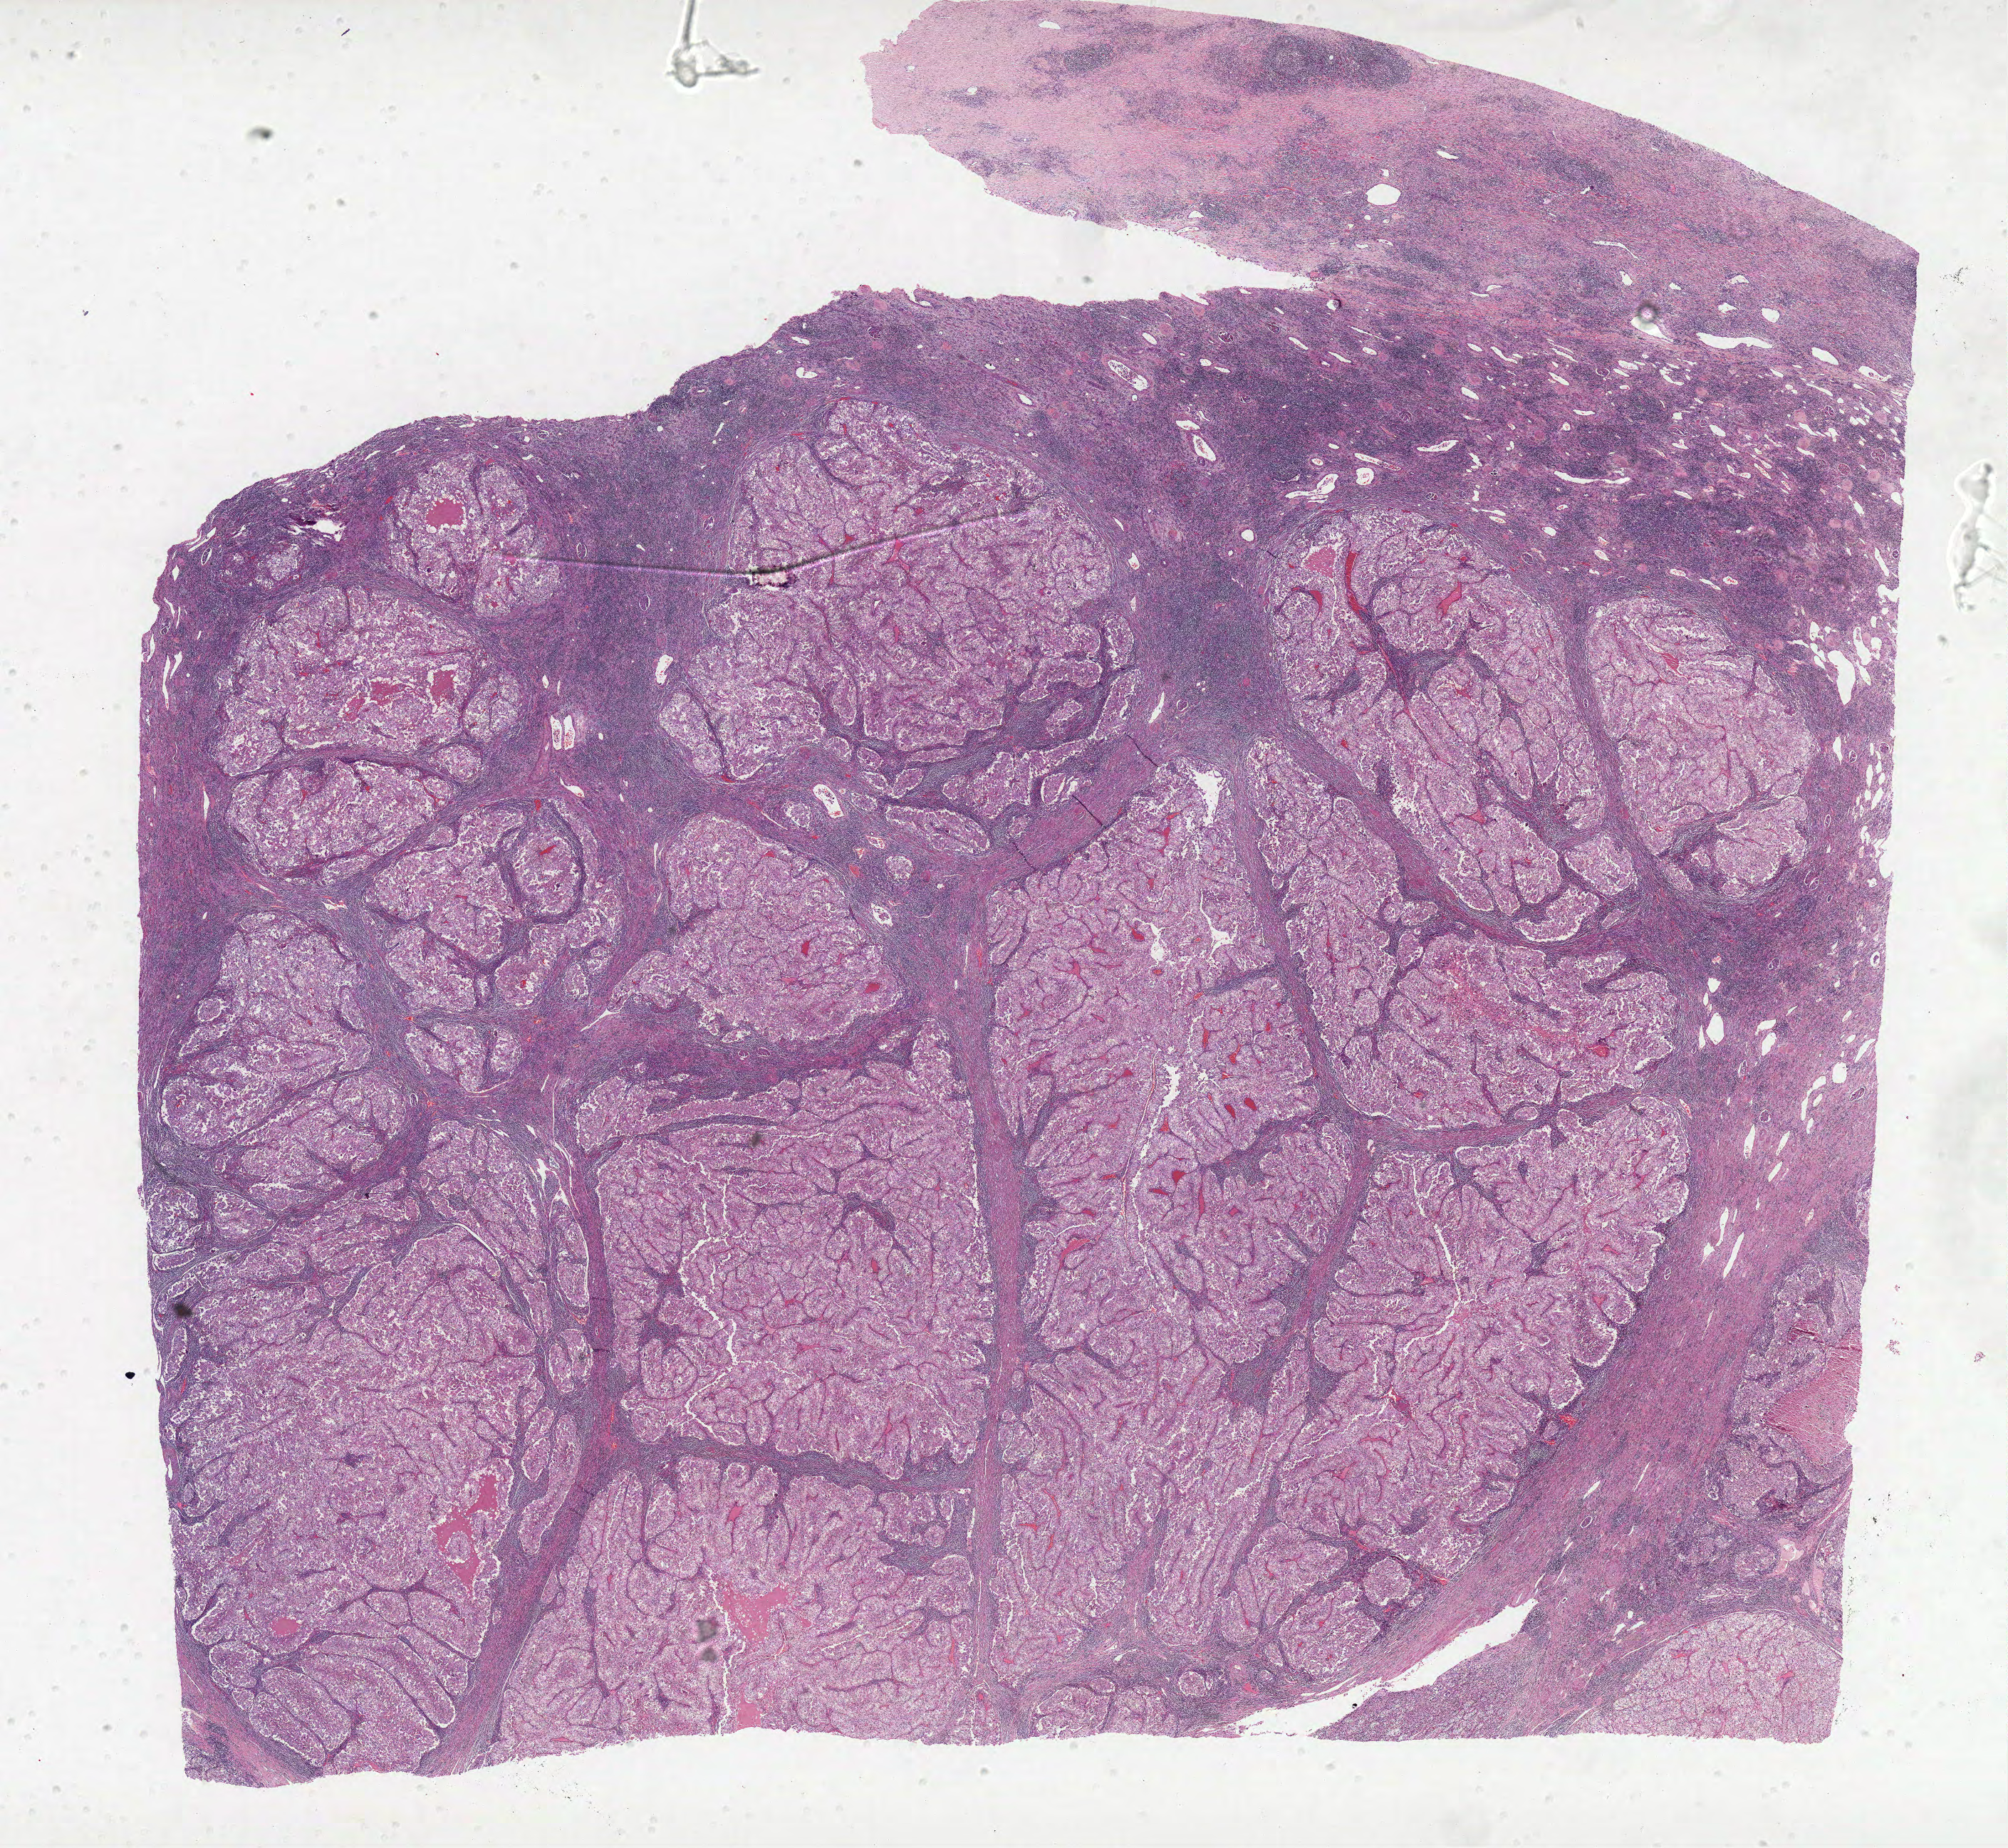
Whole-slide histology image, H&E-stained, a low-resolution overview of the entire scanned area, about 22.5 x 20.7 mm, FFPE section, sample: primary tumour, kidney. Patient: male, age at initial diagnosis 57 years. Histologic grade: G4 (undifferentiated).
AJCC pathologic stage: III. Pathologic diagnosis: Clear cell adenocarcinoma, NOS. Laterality: right.